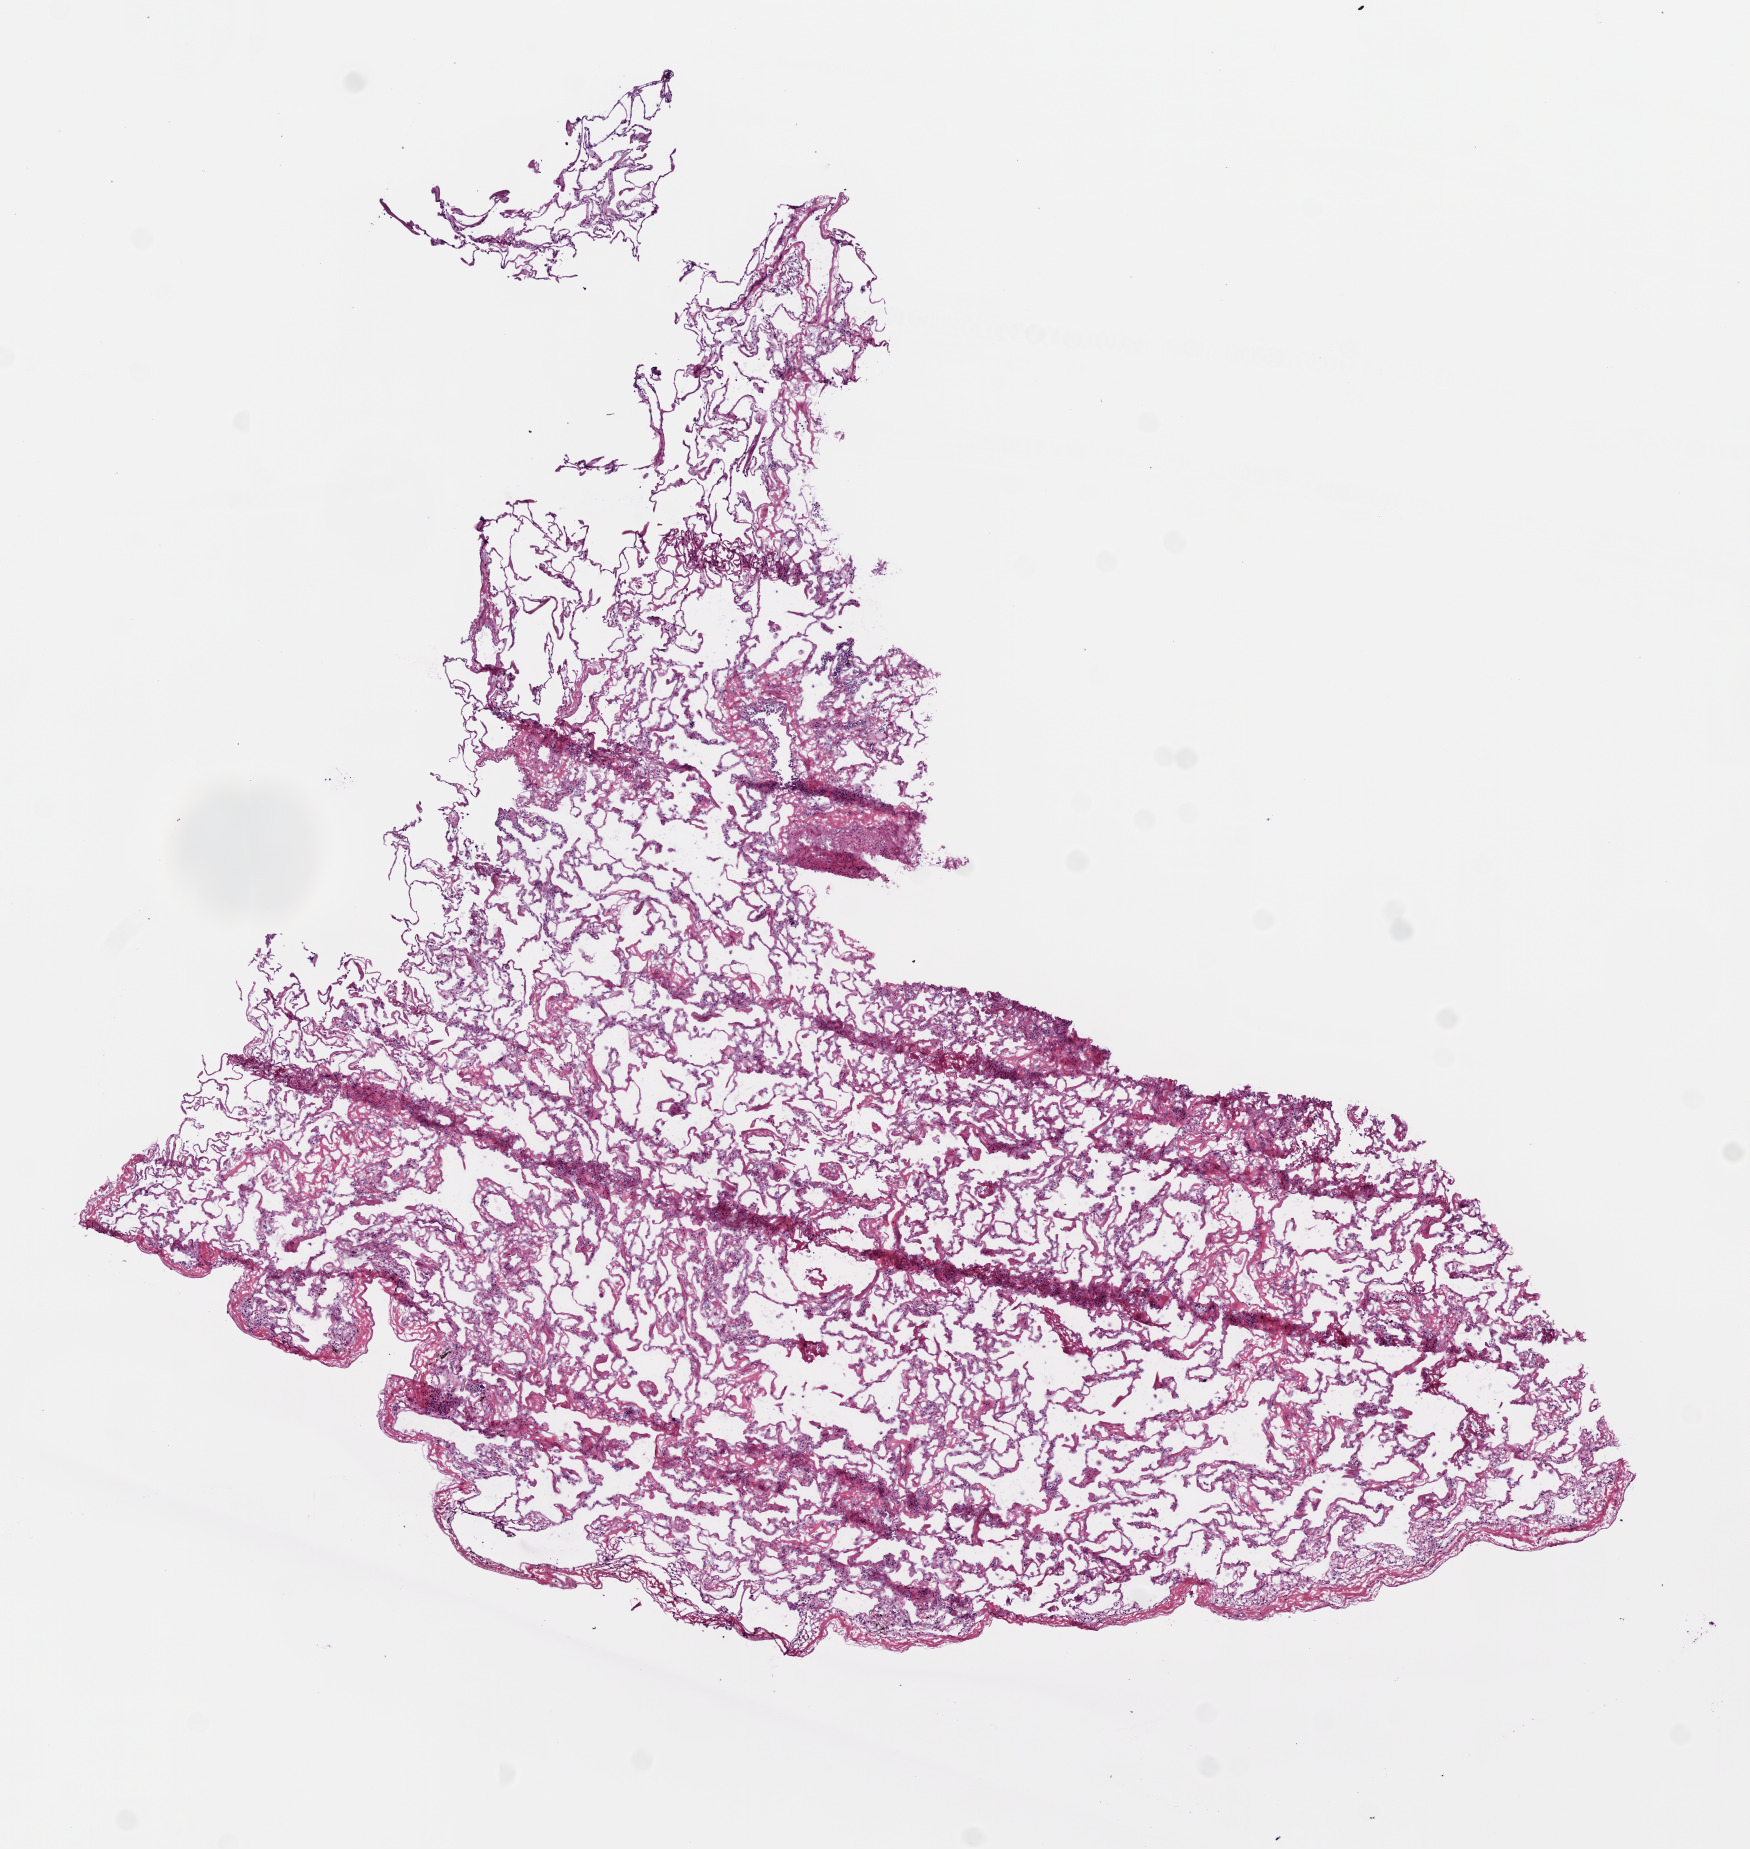
H&E whole-slide image, whole scanned area (about 7.0 x 7.4 mm, slide scanned at 20x) shown as a low-resolution overview, frozen section from the bottom of the tissue portion, solid tissue normal (non-tumour tissue) sample from the lung. Female patient; age at initial diagnosis 78 years.
This section: solid tissue normal sample (biorepository sample class). Patient diagnosis: Squamous cell carcinoma, large cell, nonkeratinizing, NOS.